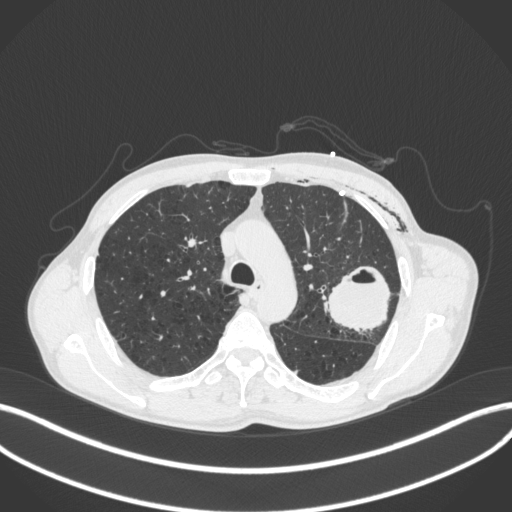
Chest CT, one axial slice; slice 285 of 416 in the series (ordered by position); reconstruction kernel B31f; 120 kVp; lung window (W 1500 / L -600 HU); 1 mm slice thickness; 512 × 512 image matrix, field of view 400 × 400 mm. Male patient, age 58 years. Case-level facts recorded for this patient, not image findings: clinical TNM (as recorded): T3 N0 M0.
Outlined on this slice (rectangle marked by the reading radiologist):
- lung tumour (recorded histology: adenocarcinoma): box from (x=322, y=264) to (x=390, y=340) px